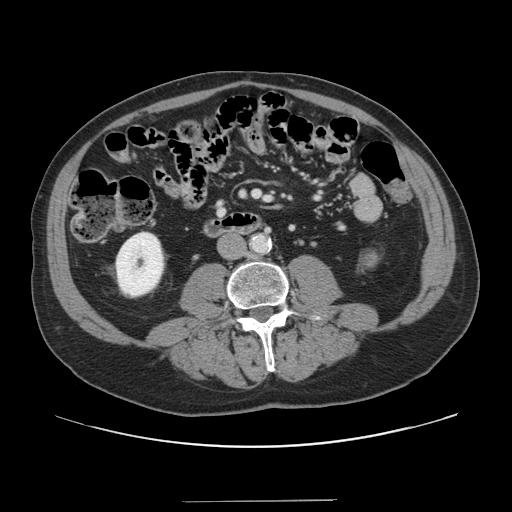
Contrast-enhanced abdominal CT, one axial slice; slice 24 of 151 in the series (ordered by position); soft-tissue window (W 400 / L 40 HU); 2.5 mm slice thickness; 512 × 512 image matrix. Male patient, age 63 years. Case-level facts recorded for this patient, not image findings: diagnosis: colorectal cancer liver metastases, imaged before liver resection; multiple liver metastases: no; largest metastasis: 2.1 cm; chemotherapy before resection: no.
Annotated regions visible in this slice (outlined manually by an expert reader):
- portal vein (with intrahepatic branches): box from (x=253, y=191) to (x=269, y=199) px